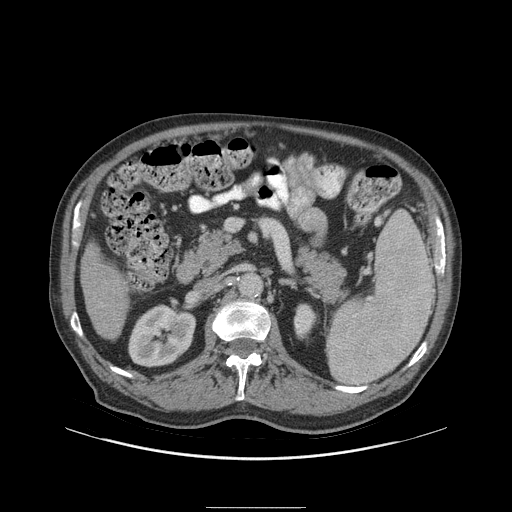
Contrast-enhanced abdominal CT (liver protocol), one axial slice; position 34 of 105 along the scan axis; soft-tissue window (W 400 / L 40 HU); 2.5 mm slice thickness; 512 × 512 image matrix, field of view 440 × 440 mm. From the clinical record (not read from this slice): diagnosis: hepatocellular carcinoma (patient treated with transarterial chemoembolisation; whether this scan precedes or follows treatment is not stated here); TNM stage (as recorded): Stage-I; Child-Pugh class: A; tumour size: 5.1 cm.
Structures marked on this image (semi-automatically segmented with operator editing):
- liver parenchyma outside the tumour (the mass and vessels are separate outlines, so this box may not span the whole liver): bounding box (x1, y1, x2, y2) in pixels: (80, 242, 130, 340)